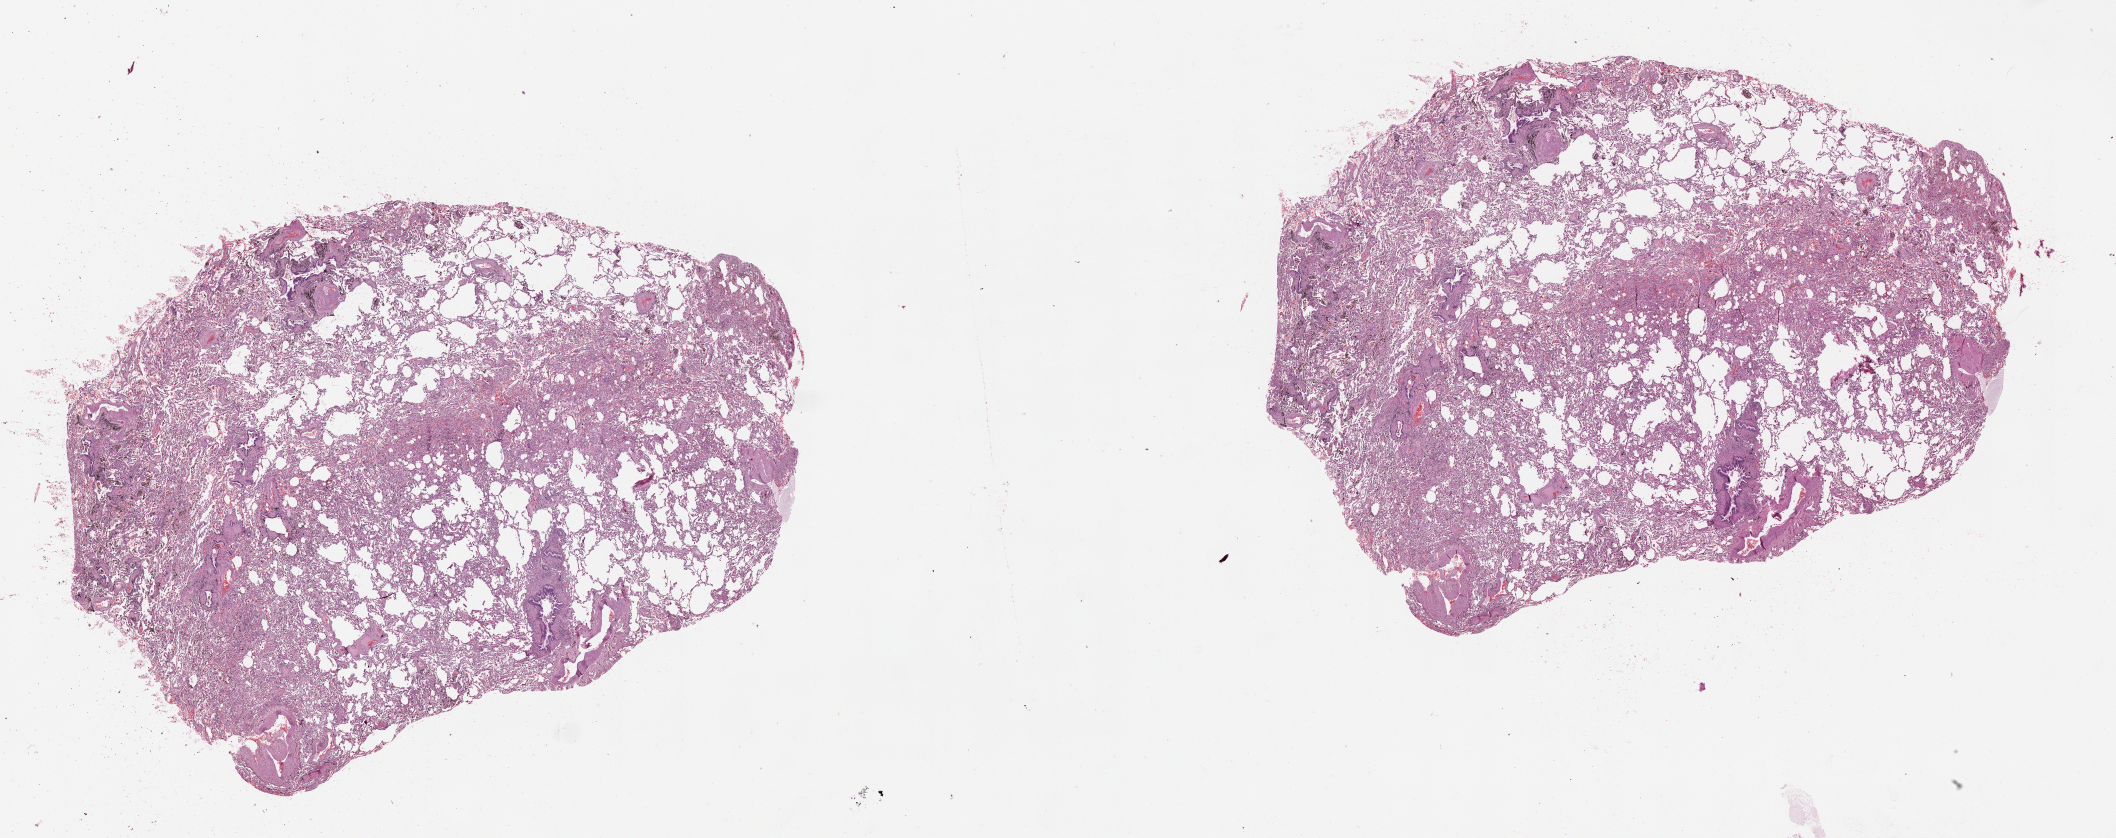
Hematoxylin and eosin (H&E) stained whole-slide image, low-resolution overview of the scanned area, about 34.1 x 13.5 mm (acquisition: 20x scan), normal (non-tumour) tissue sample, lung. Male, 59 y/o.
• this section: normal (non-tumour) tissue from the same patient
• patient diagnosis (cohort enrolment): squamous cell carcinoma (lung)